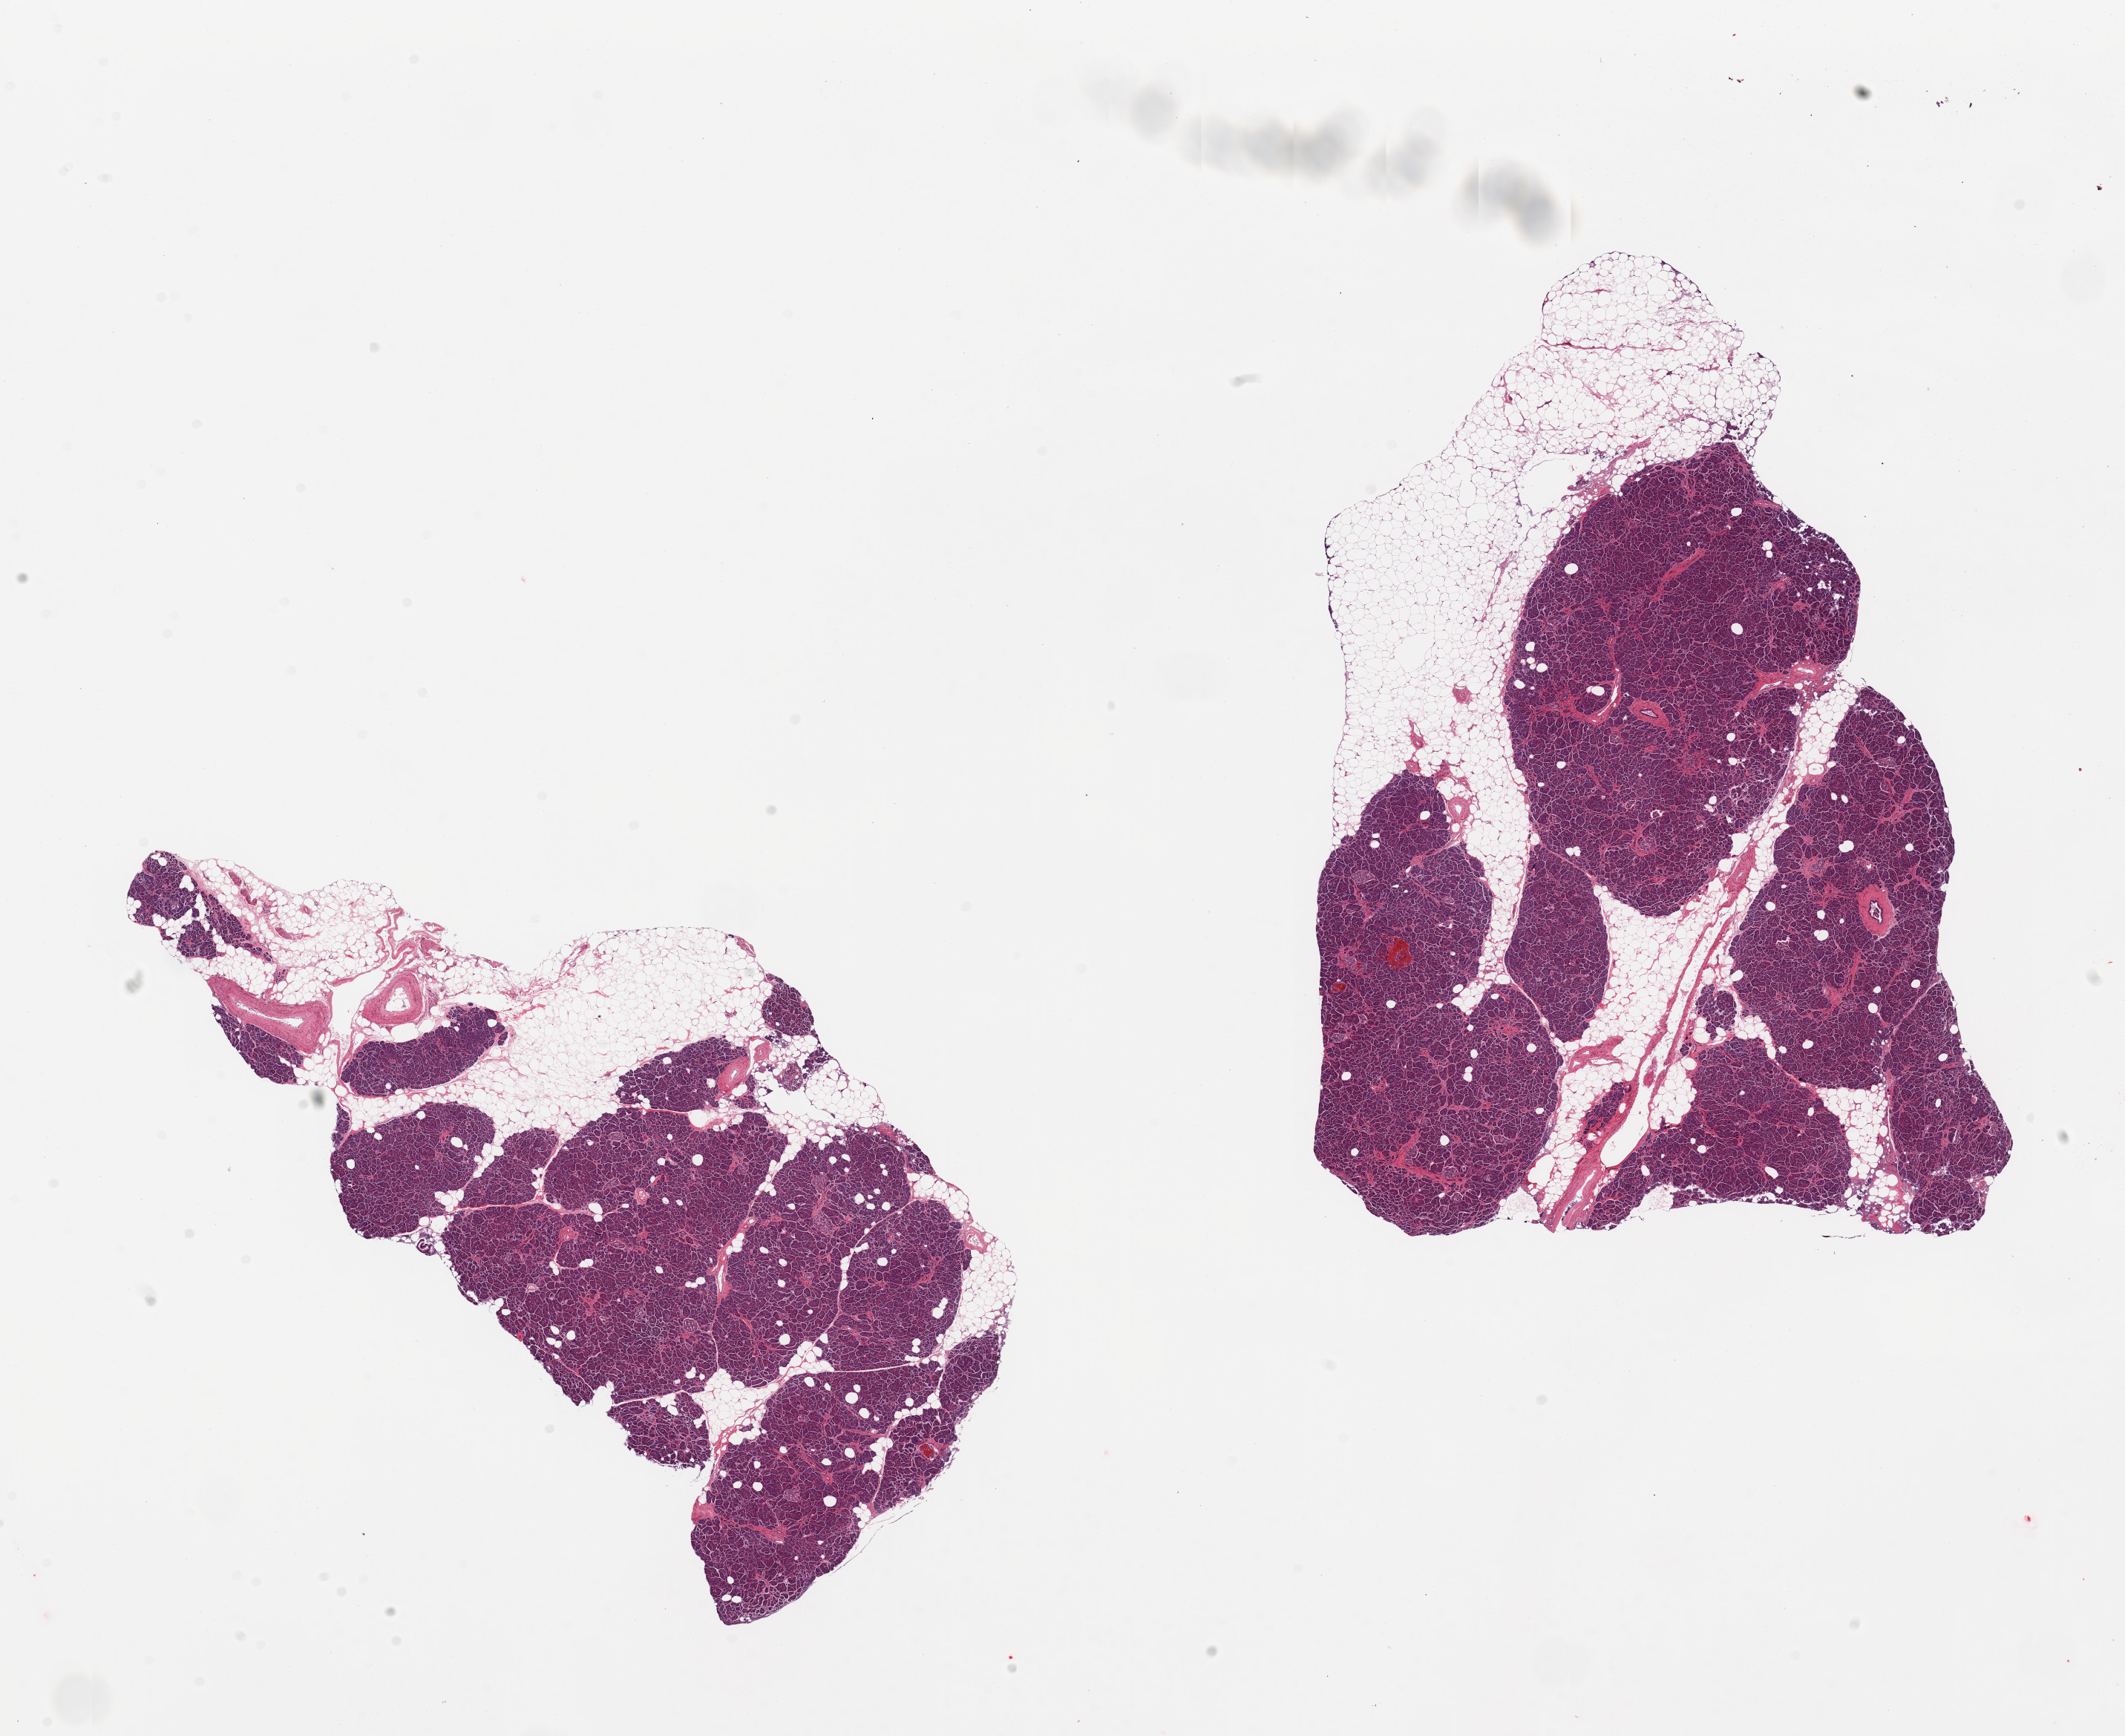
Whole-slide image, haematoxylin and eosin stain, brightfield, whole scanned area (about 22.6 x 18.5 mm) shown as a low-resolution overview; PAXgene-fixed paraffin-embedded (PFPE) section; target tissue: pancreas; tissue donor sample. Donor: male.
Reviewer comment on this tissue sample: 2 pieces, approaching score 2 for autolysis...80% pancreatic parenchyma; rest adherent fat; Islets fairly well preserved.